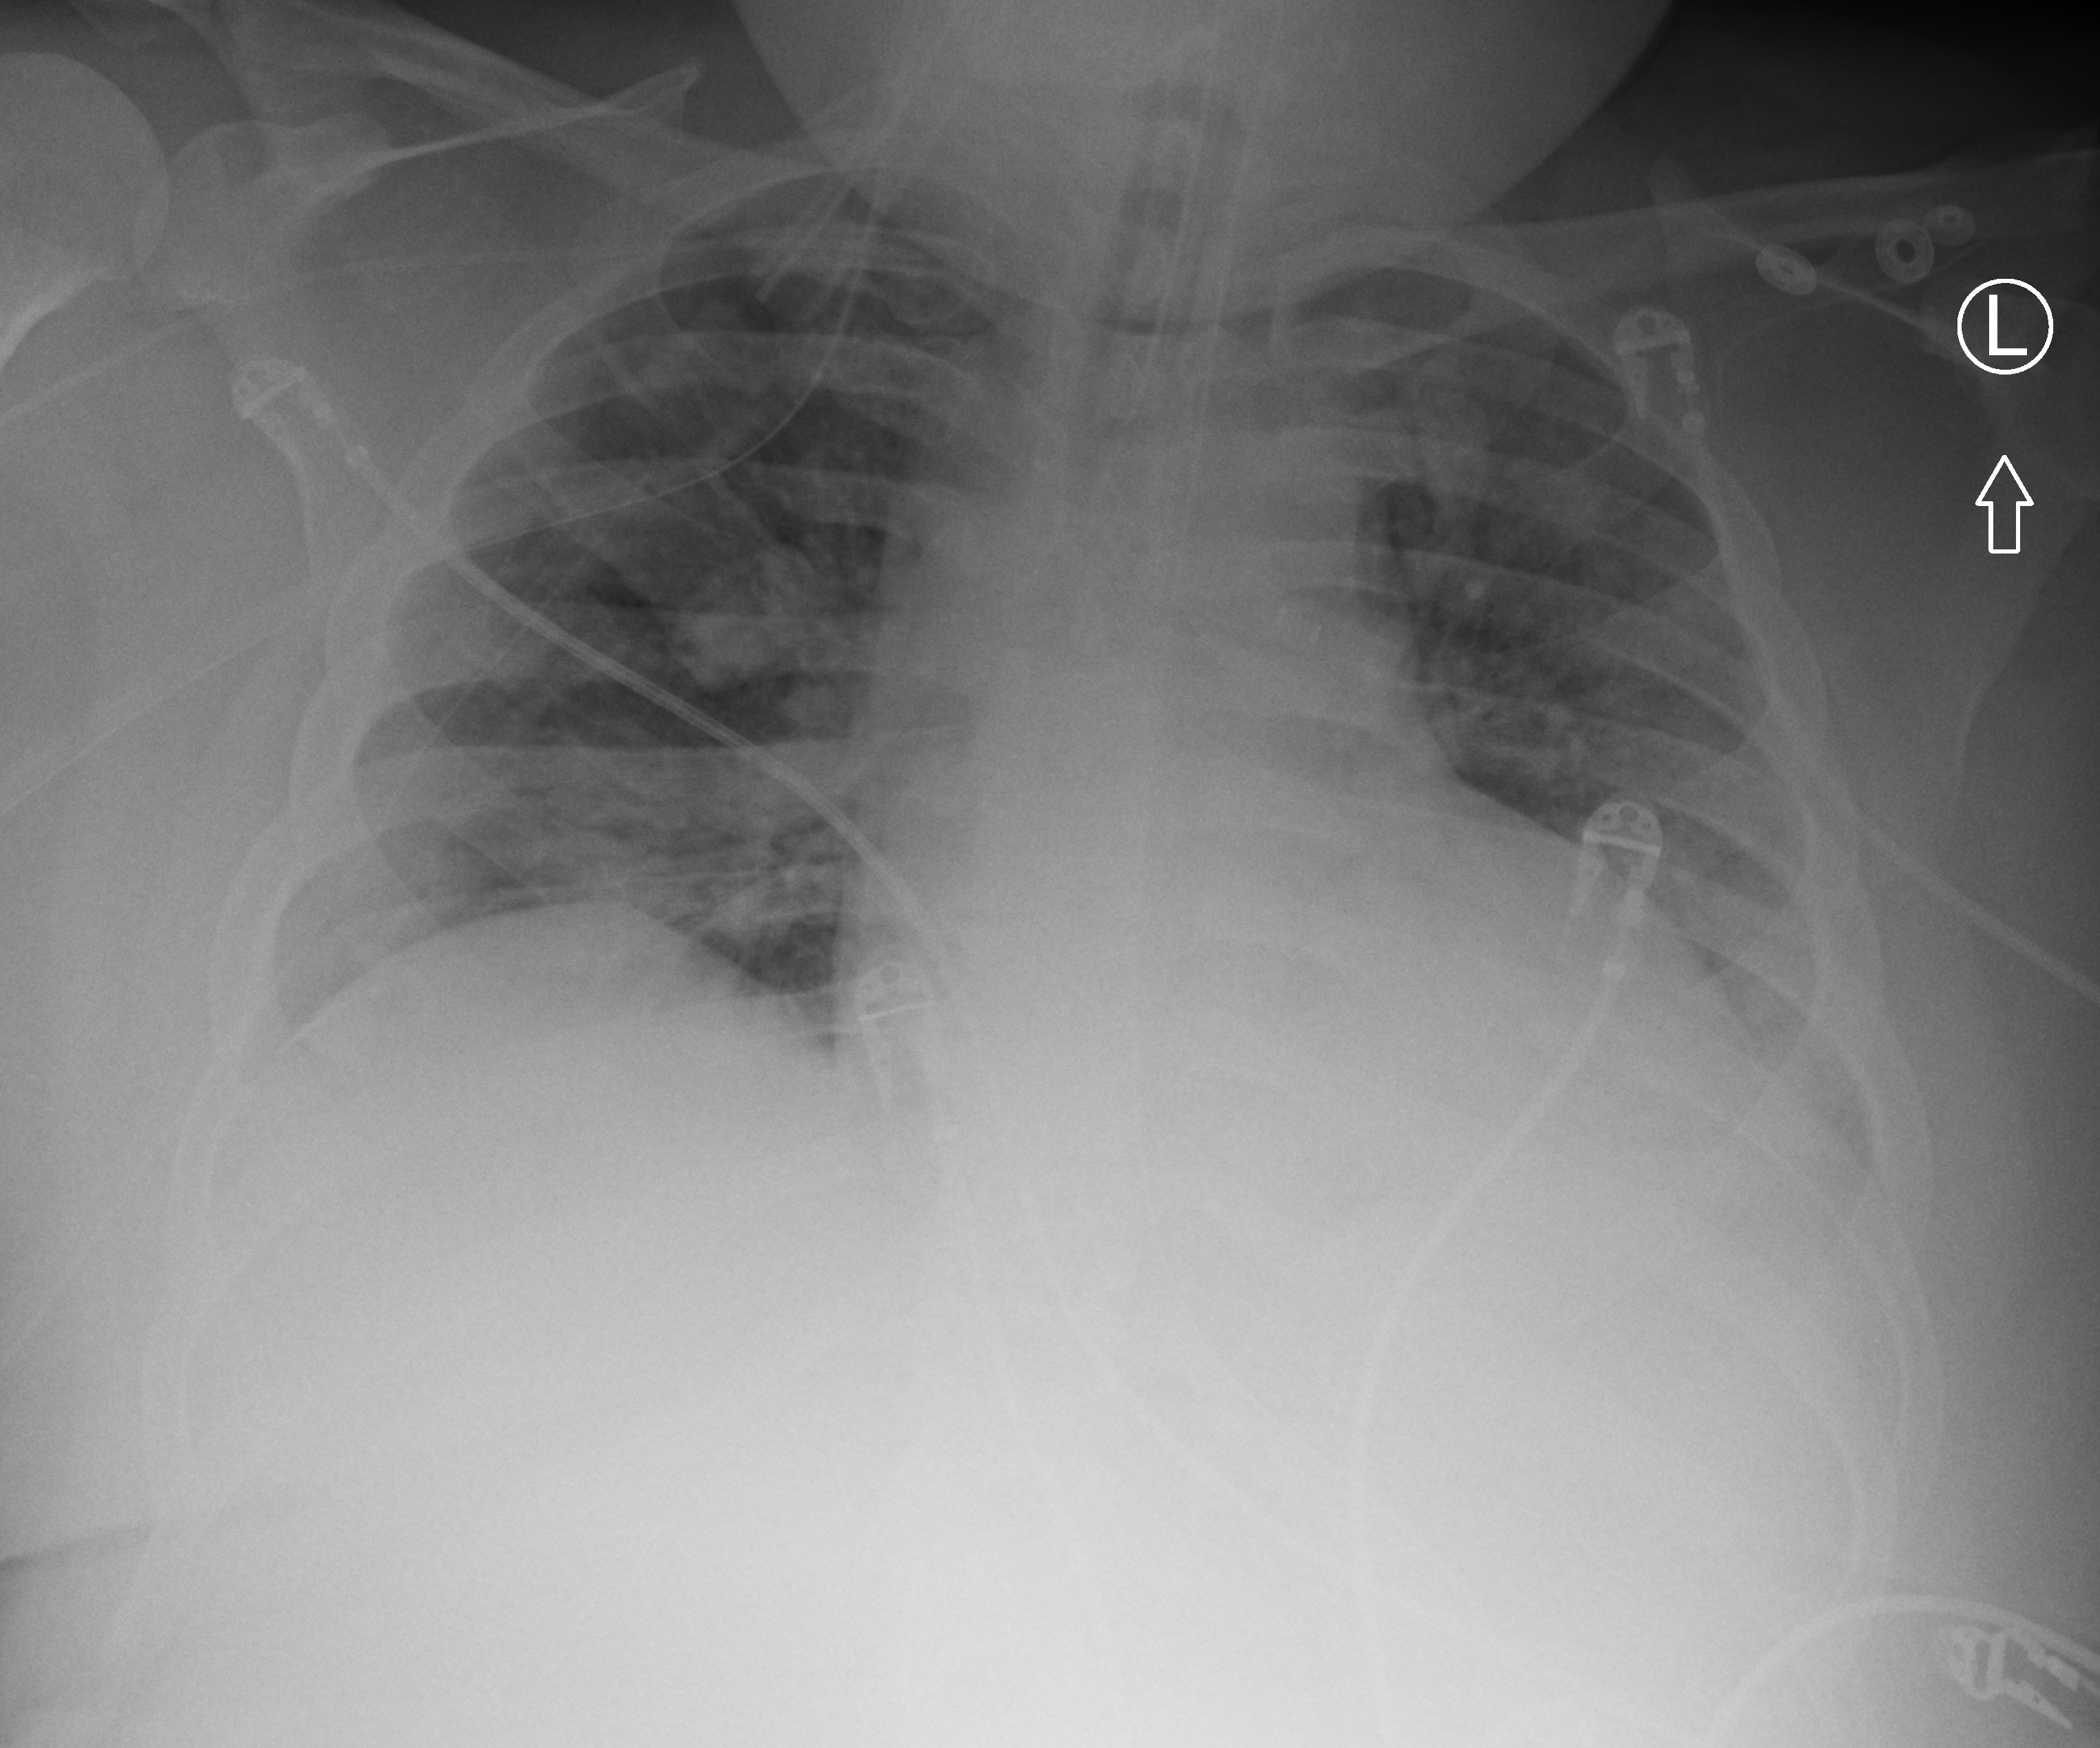
Portable chest radiograph, anteroposterior (AP) projection. Patient hospitalised with COVID-19, aged 18–59 years.
Hospital-stay facts (about this admission, not read from this image; timing relative to this image not recorded):
- mechanically ventilated during this hospital stay: yes
- admitted to intensive care during this hospital stay: yes